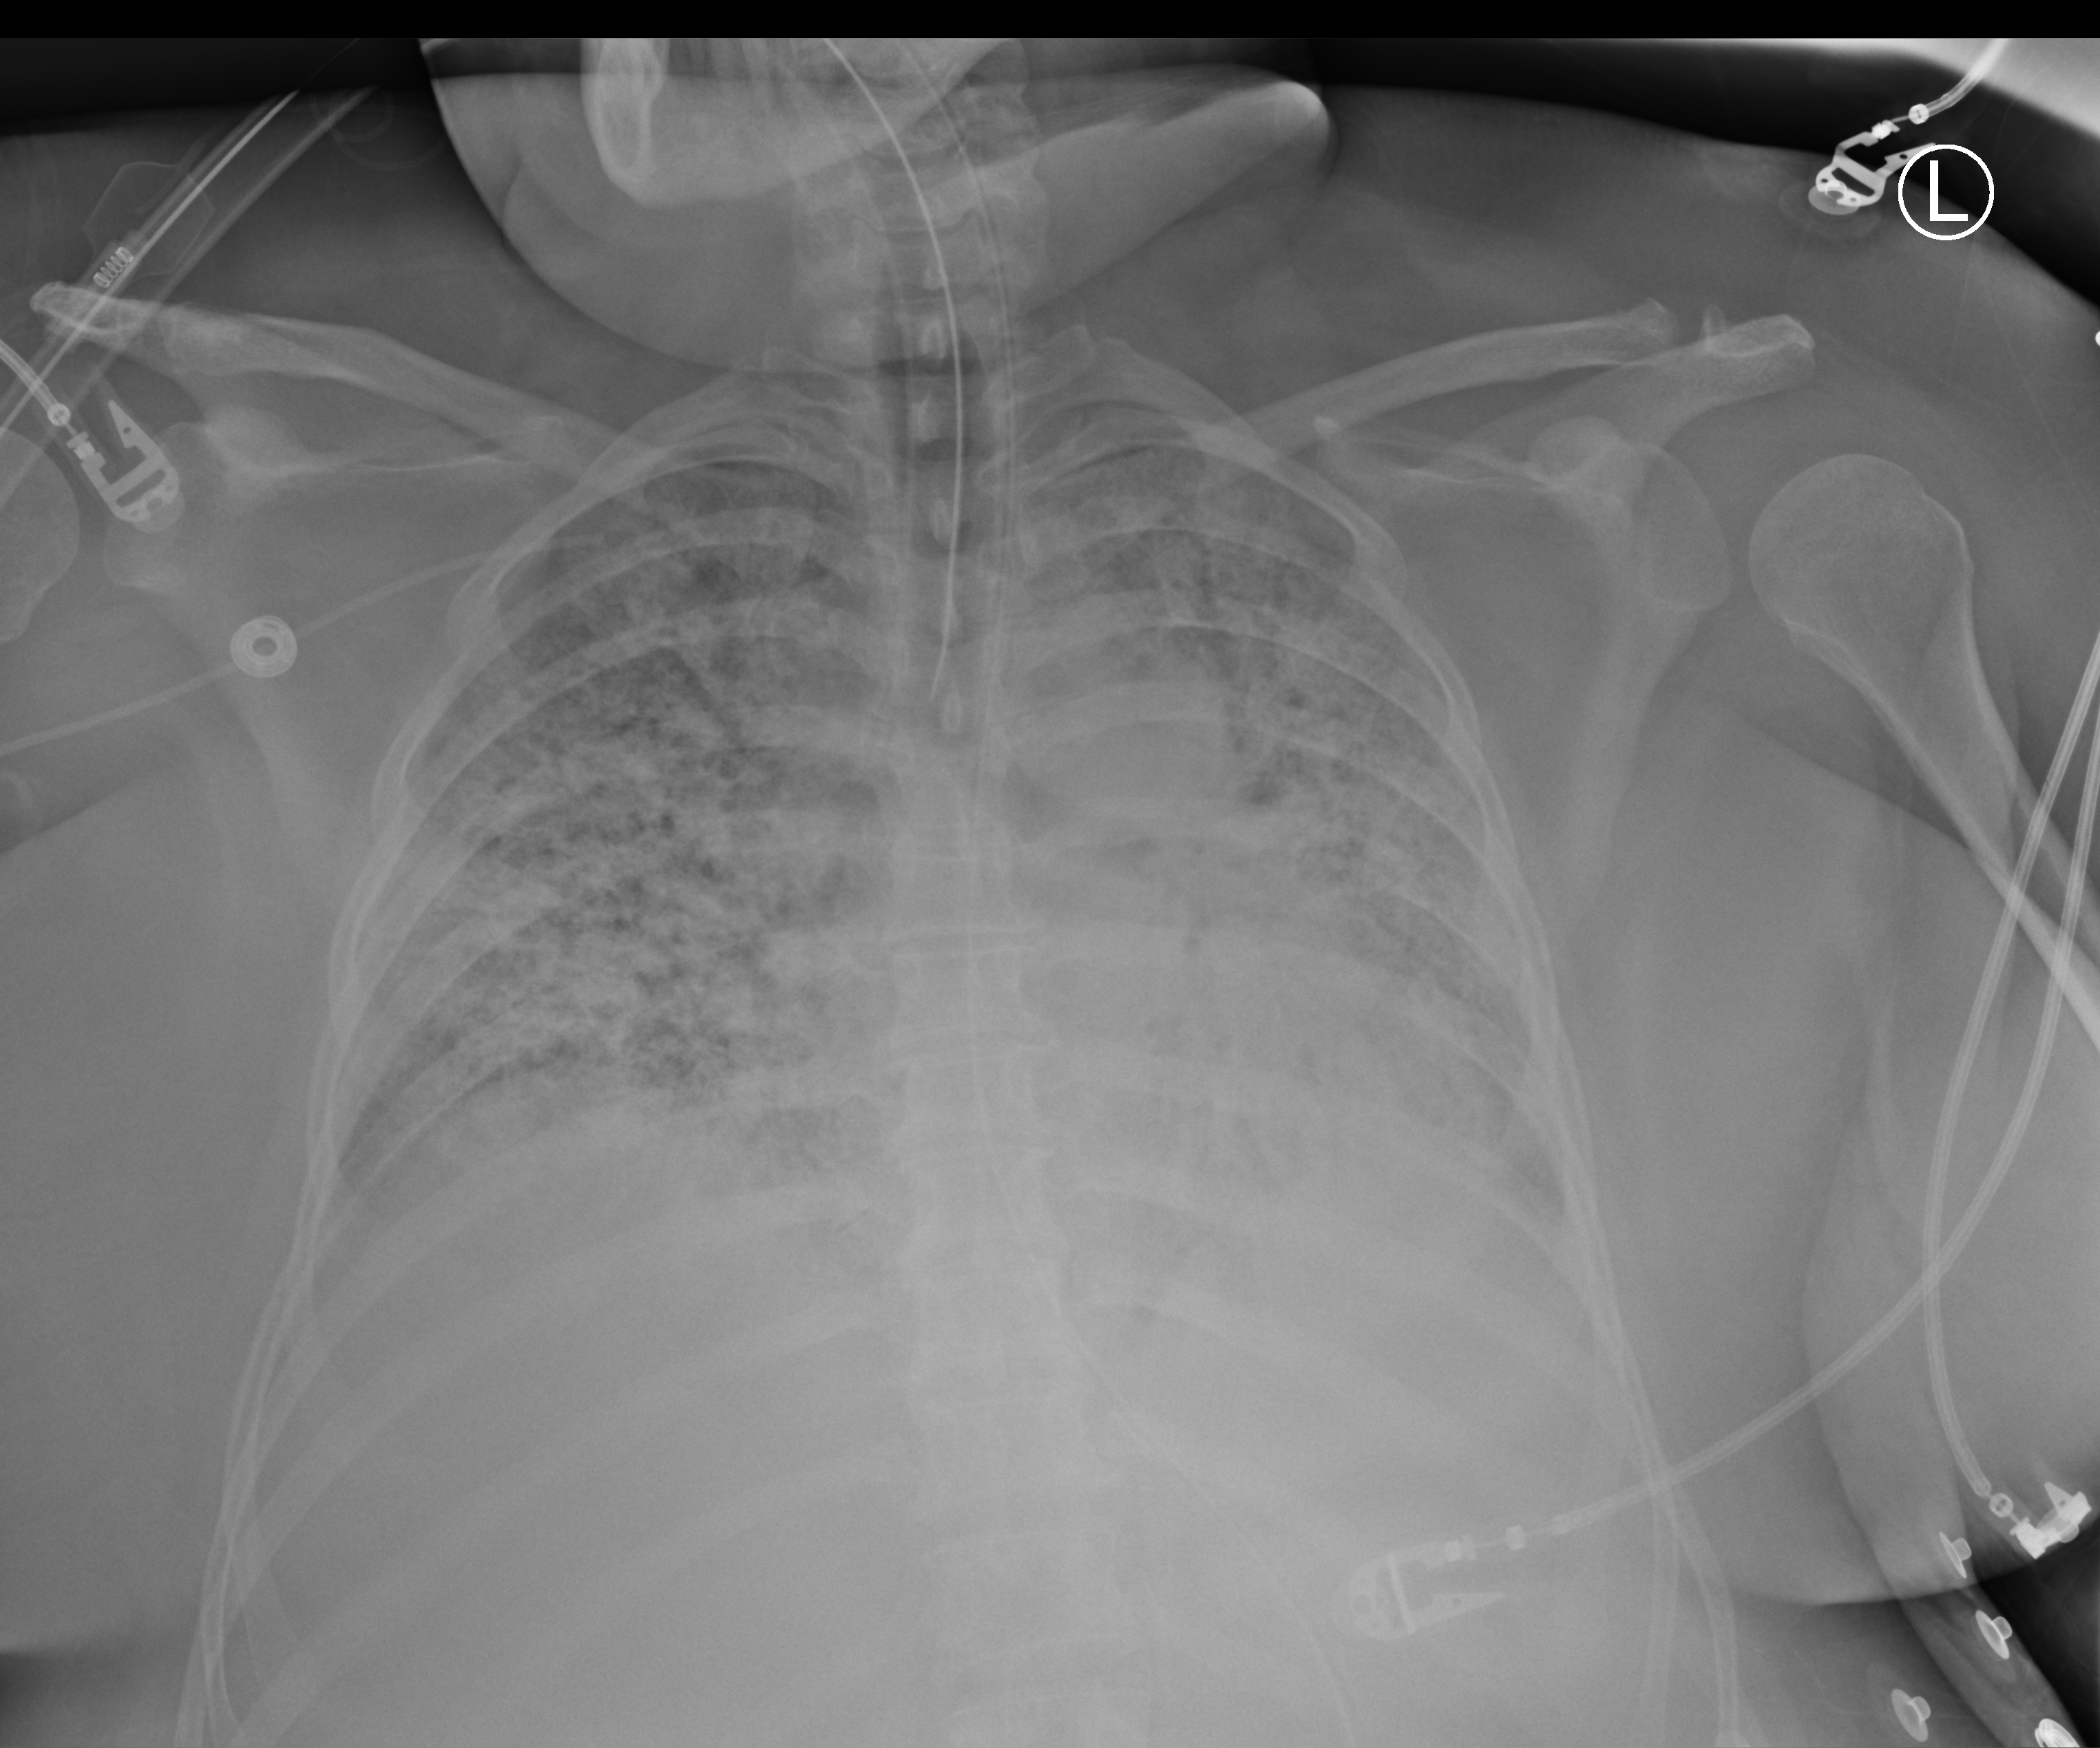
Bedside chest radiograph (computed radiography), anteroposterior (AP) projection. Female patient hospitalised with COVID-19, age 18–59 years.
From the hospital-stay record, not from the radiograph (when in the stay this image was taken is not recorded):
- chronic kidney disease (admission record): no
- mechanically ventilated during this hospital stay: yes